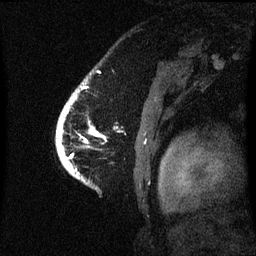
Breast MRI (dynamic contrast-enhanced), one sagittal slice. Position 51 of 60 along the scan axis. Dynamic contrast-enhanced series, image 2 of 3 at this slice position (ordered by acquisition). 1.5 T. TE 4.2 ms, TR 8.4 ms. 2.1 mm slice thickness. 256 × 256 image matrix, field of view 220 × 220 mm. Patient: female, 53 years. From the clinical record (not read from this slice): setting: breast cancer imaged before/during neoadjuvant chemotherapy; receptor status: HR-positive, HER2-negative.
Structures marked on this image (semi-automatic segmentation, software-assisted and operator-edited):
- analysis volume of interest (the breast-tissue region the enhancement analysis was run in; not a lesion): box from (x=57, y=92) to (x=106, y=171) px
- tumour enhancement mask (voxels above the 70 % enhancement threshold inside the analysis volume of interest): (x=60, y=106)–(x=101, y=137)